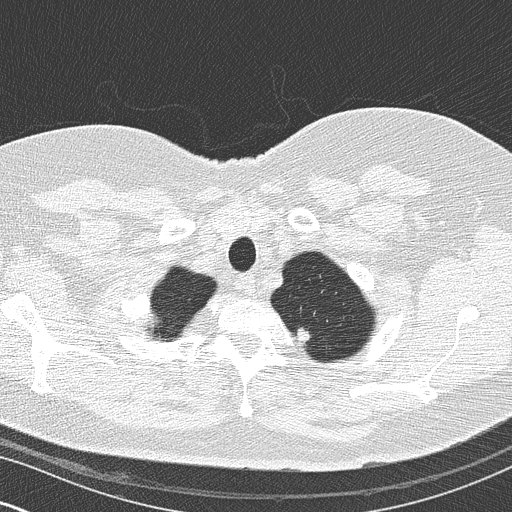
Axial slice from a low-dose chest CT screening exam; second annual screen; lung window (W 1500 / L -600 HU); 2 mm slice thickness; lung (sharp) reconstruction kernel (B50f); 512 × 512 image matrix, field of view 320 × 320 mm. Female, age 60 years at enrolment.
- Lesion marked by an expert reader, bounding box [x1, y1, x2, y2] px = [278, 319, 323, 360].
- No non-calcified nodule or mass ≥4 mm was recorded by the screening reader at this exam.
- Official screen result: negative screen, minor abnormalities not suspicious for lung cancer.
- Lung cancer was diagnosed 464 days after this screen: non-small cell carcinoma, left upper lobe, poorly differentiated (G3), stage IB (AJCC 6th edition), 16 mm at pathology.